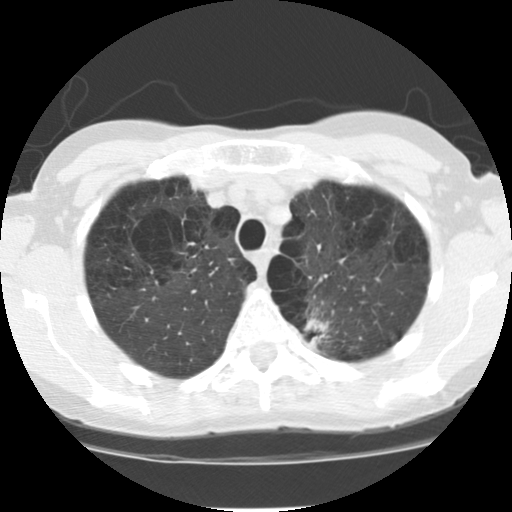
Low-dose screening chest CT, one axial slice. Slice 93 of 116 in the series (ordered by position). Reconstruction kernel STANDARD. Lung window (W 1500 / L -600 HU). 2.5 mm slice thickness. 512 × 512 image matrix.
Annotated regions visible in this slice (manually delineated by an expert):
- lesion 1 (tumor, upper lobe of left lung): bounding box [x1, y1, x2, y2] px = [304, 311, 329, 347]